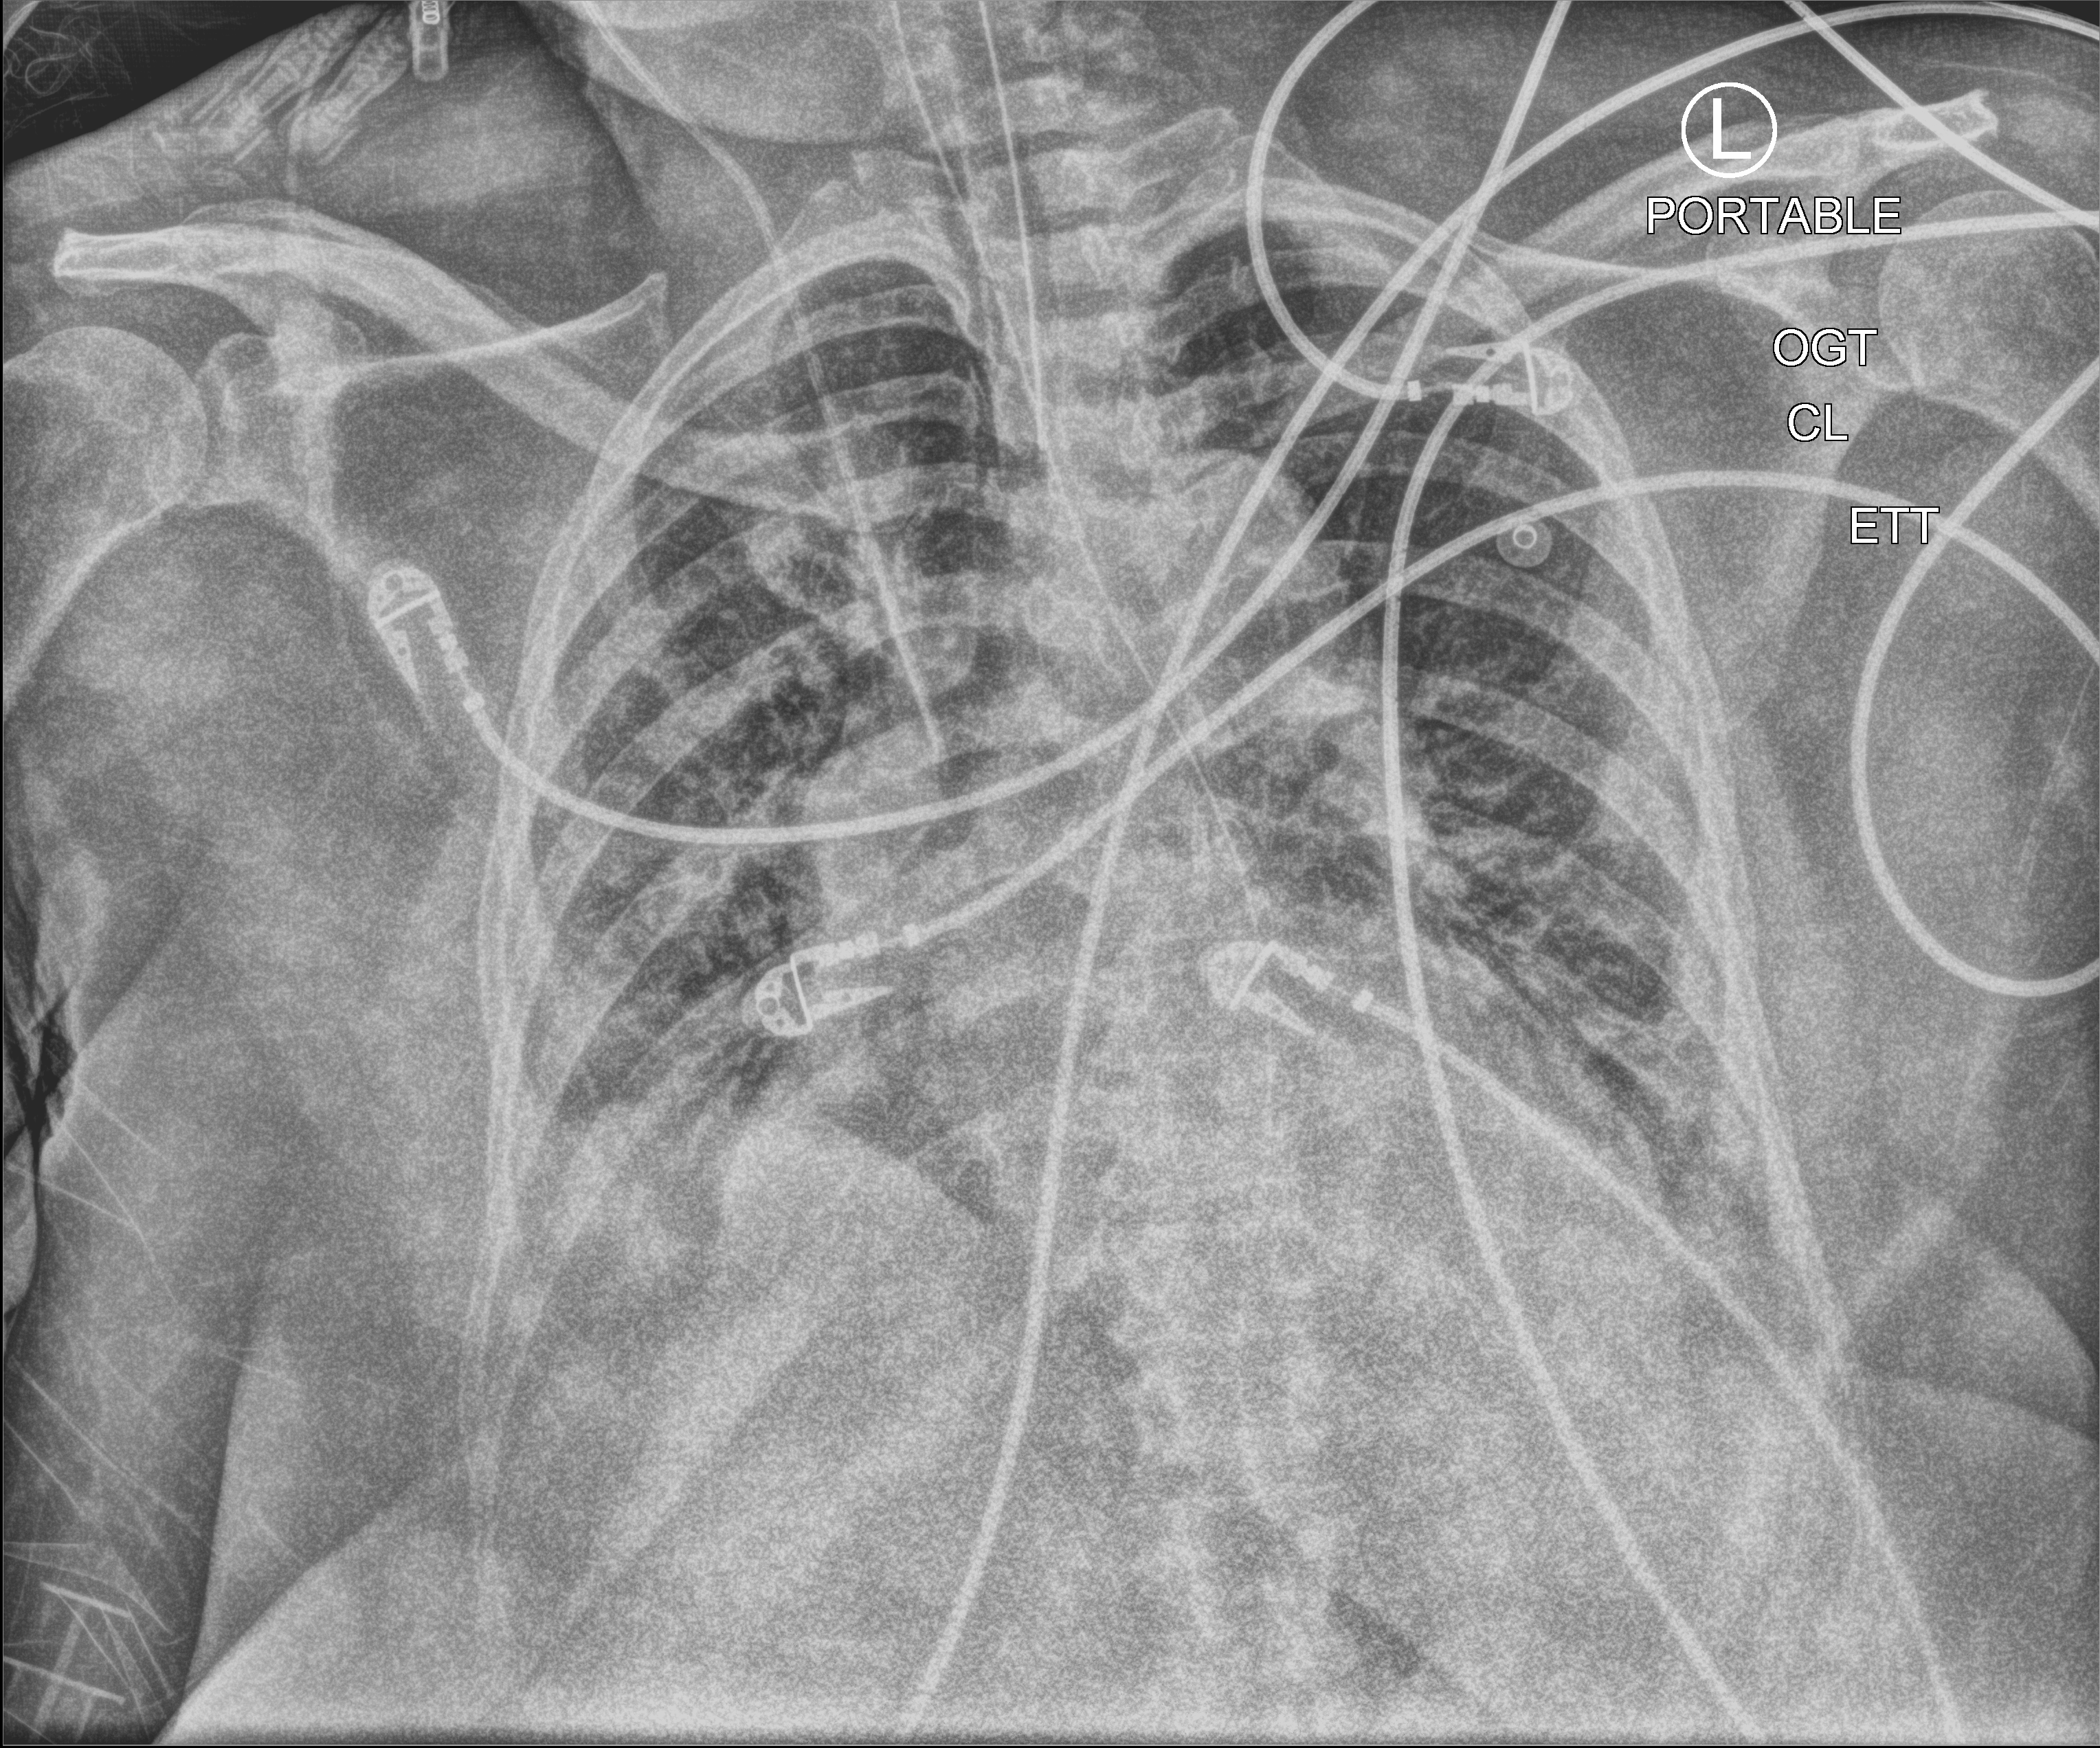
Chest X-ray (portable), anteroposterior (AP) projection. Patient hospitalised with COVID-19; female, aged 60–74 years.
Admission-level facts for this patient (not findings on this image; timing relative to this image not recorded): mechanically ventilated during this hospital stay: yes; admitted to intensive care during this hospital stay: yes.